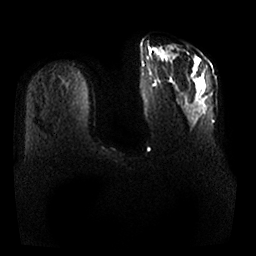
Breast MRI, one axial slice. Position 5 of 25 along the scan axis. Diffusion-weighted series; image 2 of 4 stored at this slice position (different b-values; order by instance number). 1.5 T. 4 mm slice thickness. 256 × 256 image matrix, field of view 380 × 380 mm. Female patient.
Outlined on this slice (expert manual segmentation):
- tumour on diffusion-weighted imaging: bounding box <158,49,205,89> (left, top, right, bottom; pixels)